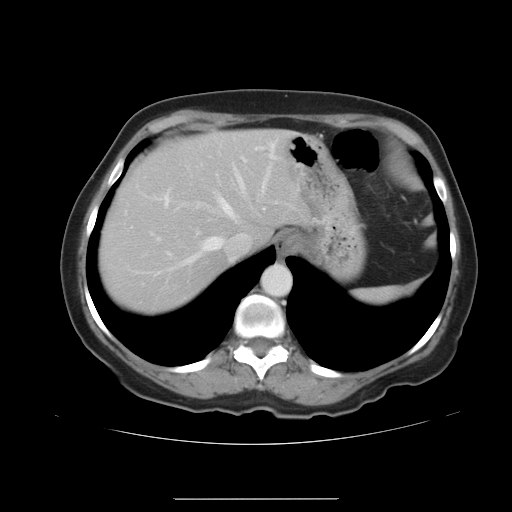
Contrast-enhanced abdominal CT, one axial slice. Slice 31 of 41 in the series (ordered by position). 120 kVp. Intravenous contrast given. Soft-tissue window (W 400 / L 40 HU). 5 mm slice thickness. 512 × 512 image matrix, field of view 381 × 381 mm. Female patient, age 63 years. Case-level facts recorded for this patient, not image findings: diagnosis: colorectal cancer liver metastases, imaged before liver resection; multiple liver metastases: yes; largest metastasis: 1.5 cm; disease in both lobes: yes.
Structures marked on this image (manually delineated by an expert):
- hepatic veins: bounding box <157,164,271,274> (left, top, right, bottom; pixels)
- liver: <99,130,307,314>
- planned liver remnant (the part of the liver to remain after resection): <99,130,307,314>
- portal vein (with intrahepatic branches): <165,157,248,204>